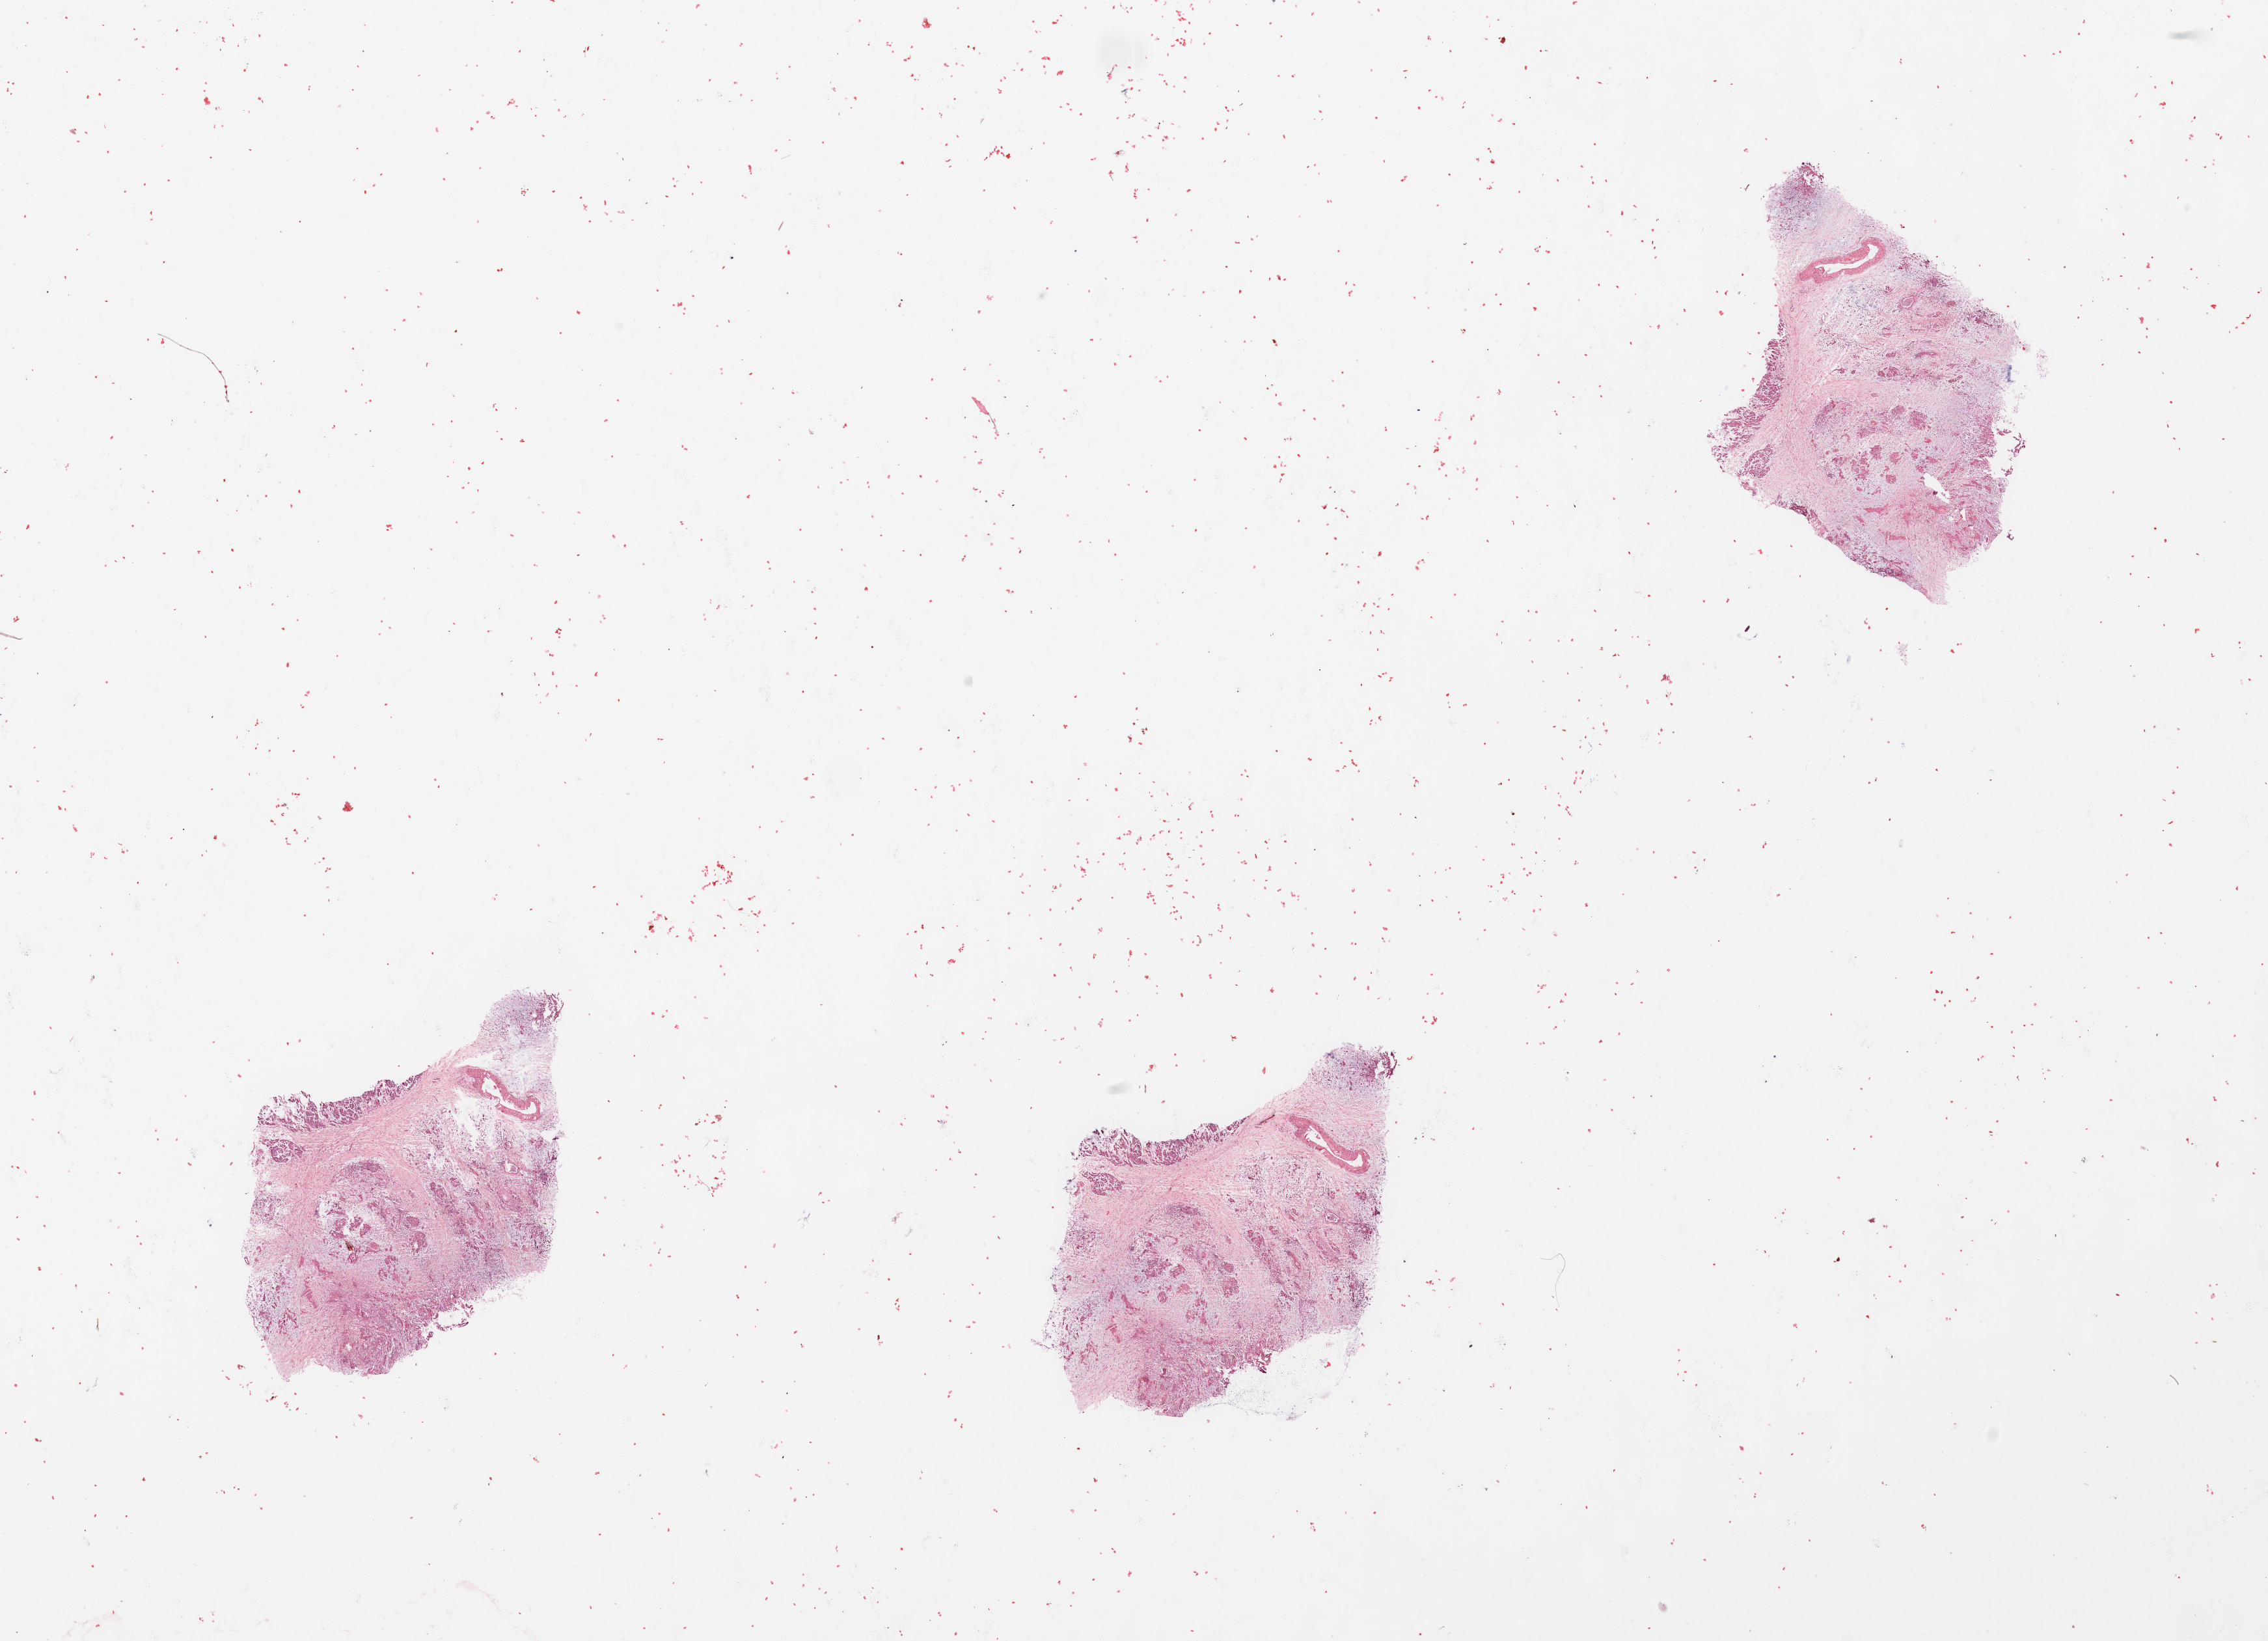
H&E whole-slide image — whole scanned area (about 27.6 x 19.9 mm, slide scanned at 20x) shown as a low-resolution overview; tumour tissue sample, pancreas. 53-year-old male patient.
Patient diagnosis (cohort enrolment): ductal adenocarcinoma (pancreas). Primary tumour site (as recorded): head.